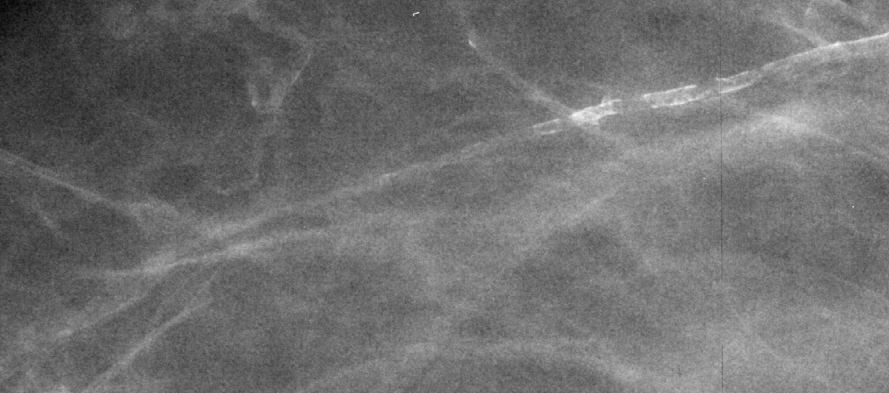
Crop from a digitized film mammogram around one marked abnormality; right breast; CC view.
Calcifications, morphology vascular; BI-RADS assessment category 2; subtlety rating 4 on a 1 (subtle) to 5 (obvious) scale; benign; no additional work-up was recommended (benign without callback).